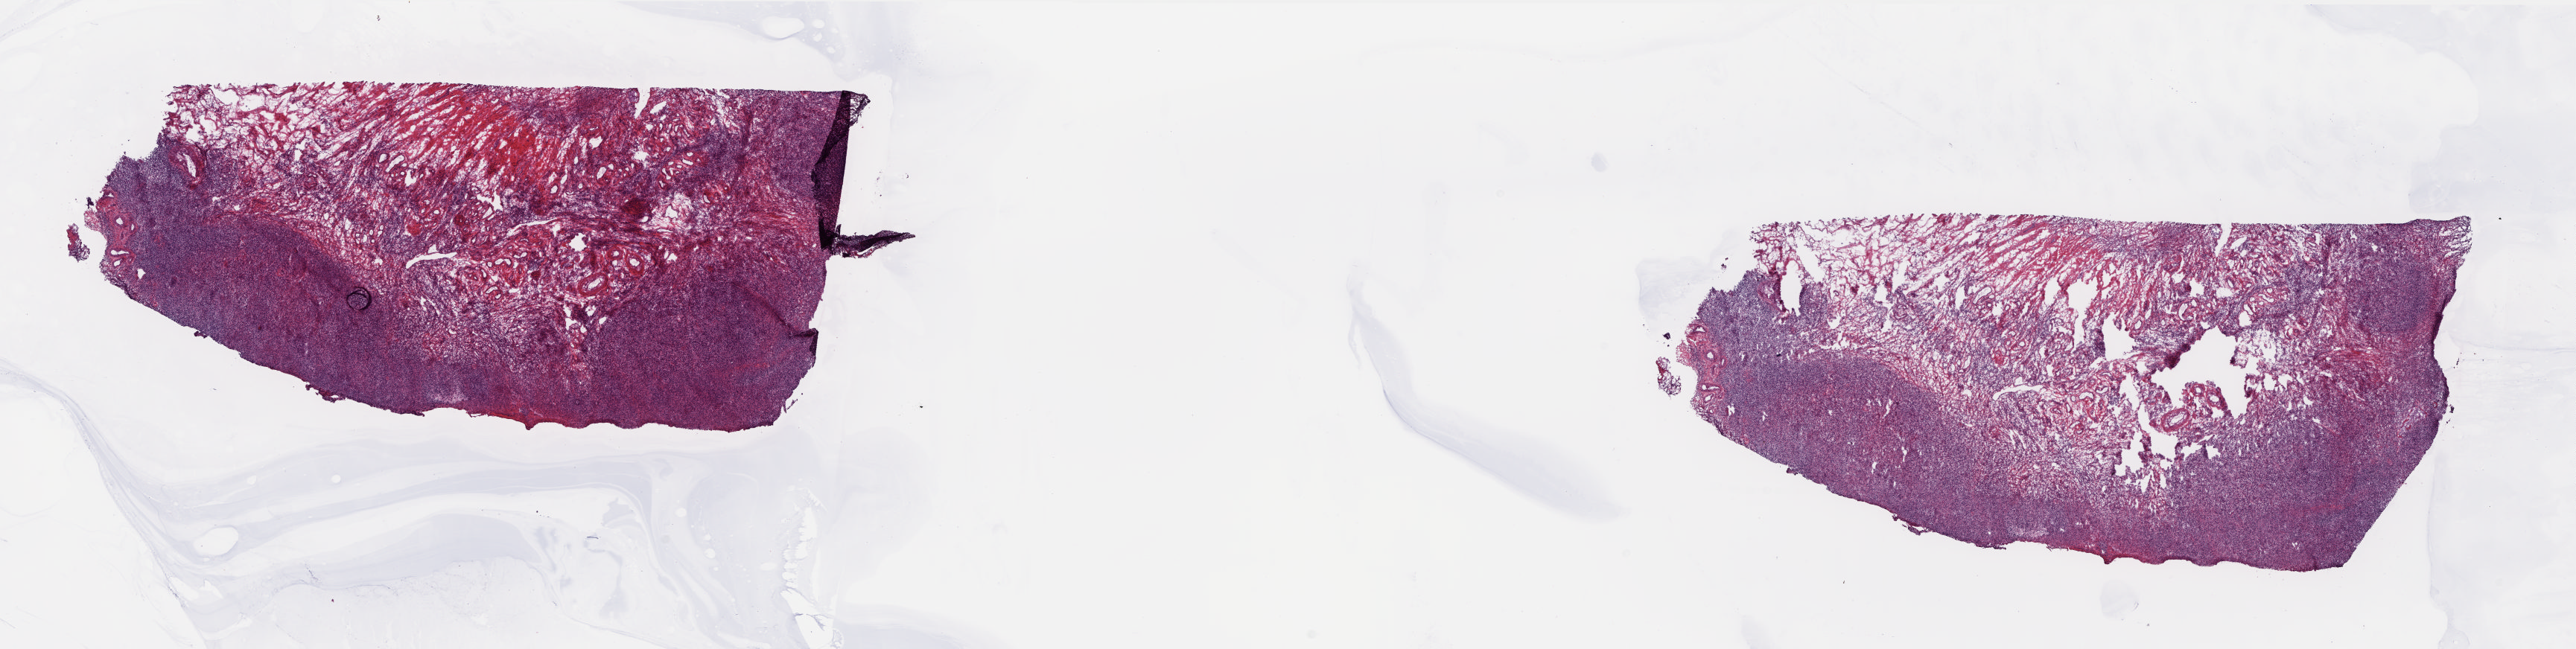
Whole-slide histology image, H&E-stained — low-resolution overview of the scanned area, about 27.9 x 7.0 mm (slide scanned at 20x), frozen section from the top of the tissue portion, sample: solid tissue normal (non-tumour tissue), uterus. Female patient; age at initial diagnosis 81 years. Slide review estimates, as recorded: tumour cells 0%, tumour nuclei 0%, normal cells 80%, stromal cells 20%, necrosis 0%. Inflammatory infiltration, as recorded: lymphocyte infiltration 0%, monocyte infiltration 0%, neutrophil infiltration 0%.
This section: solid tissue normal sample (biorepository sample class). Patient diagnosis: Mullerian mixed tumor (endometrium).